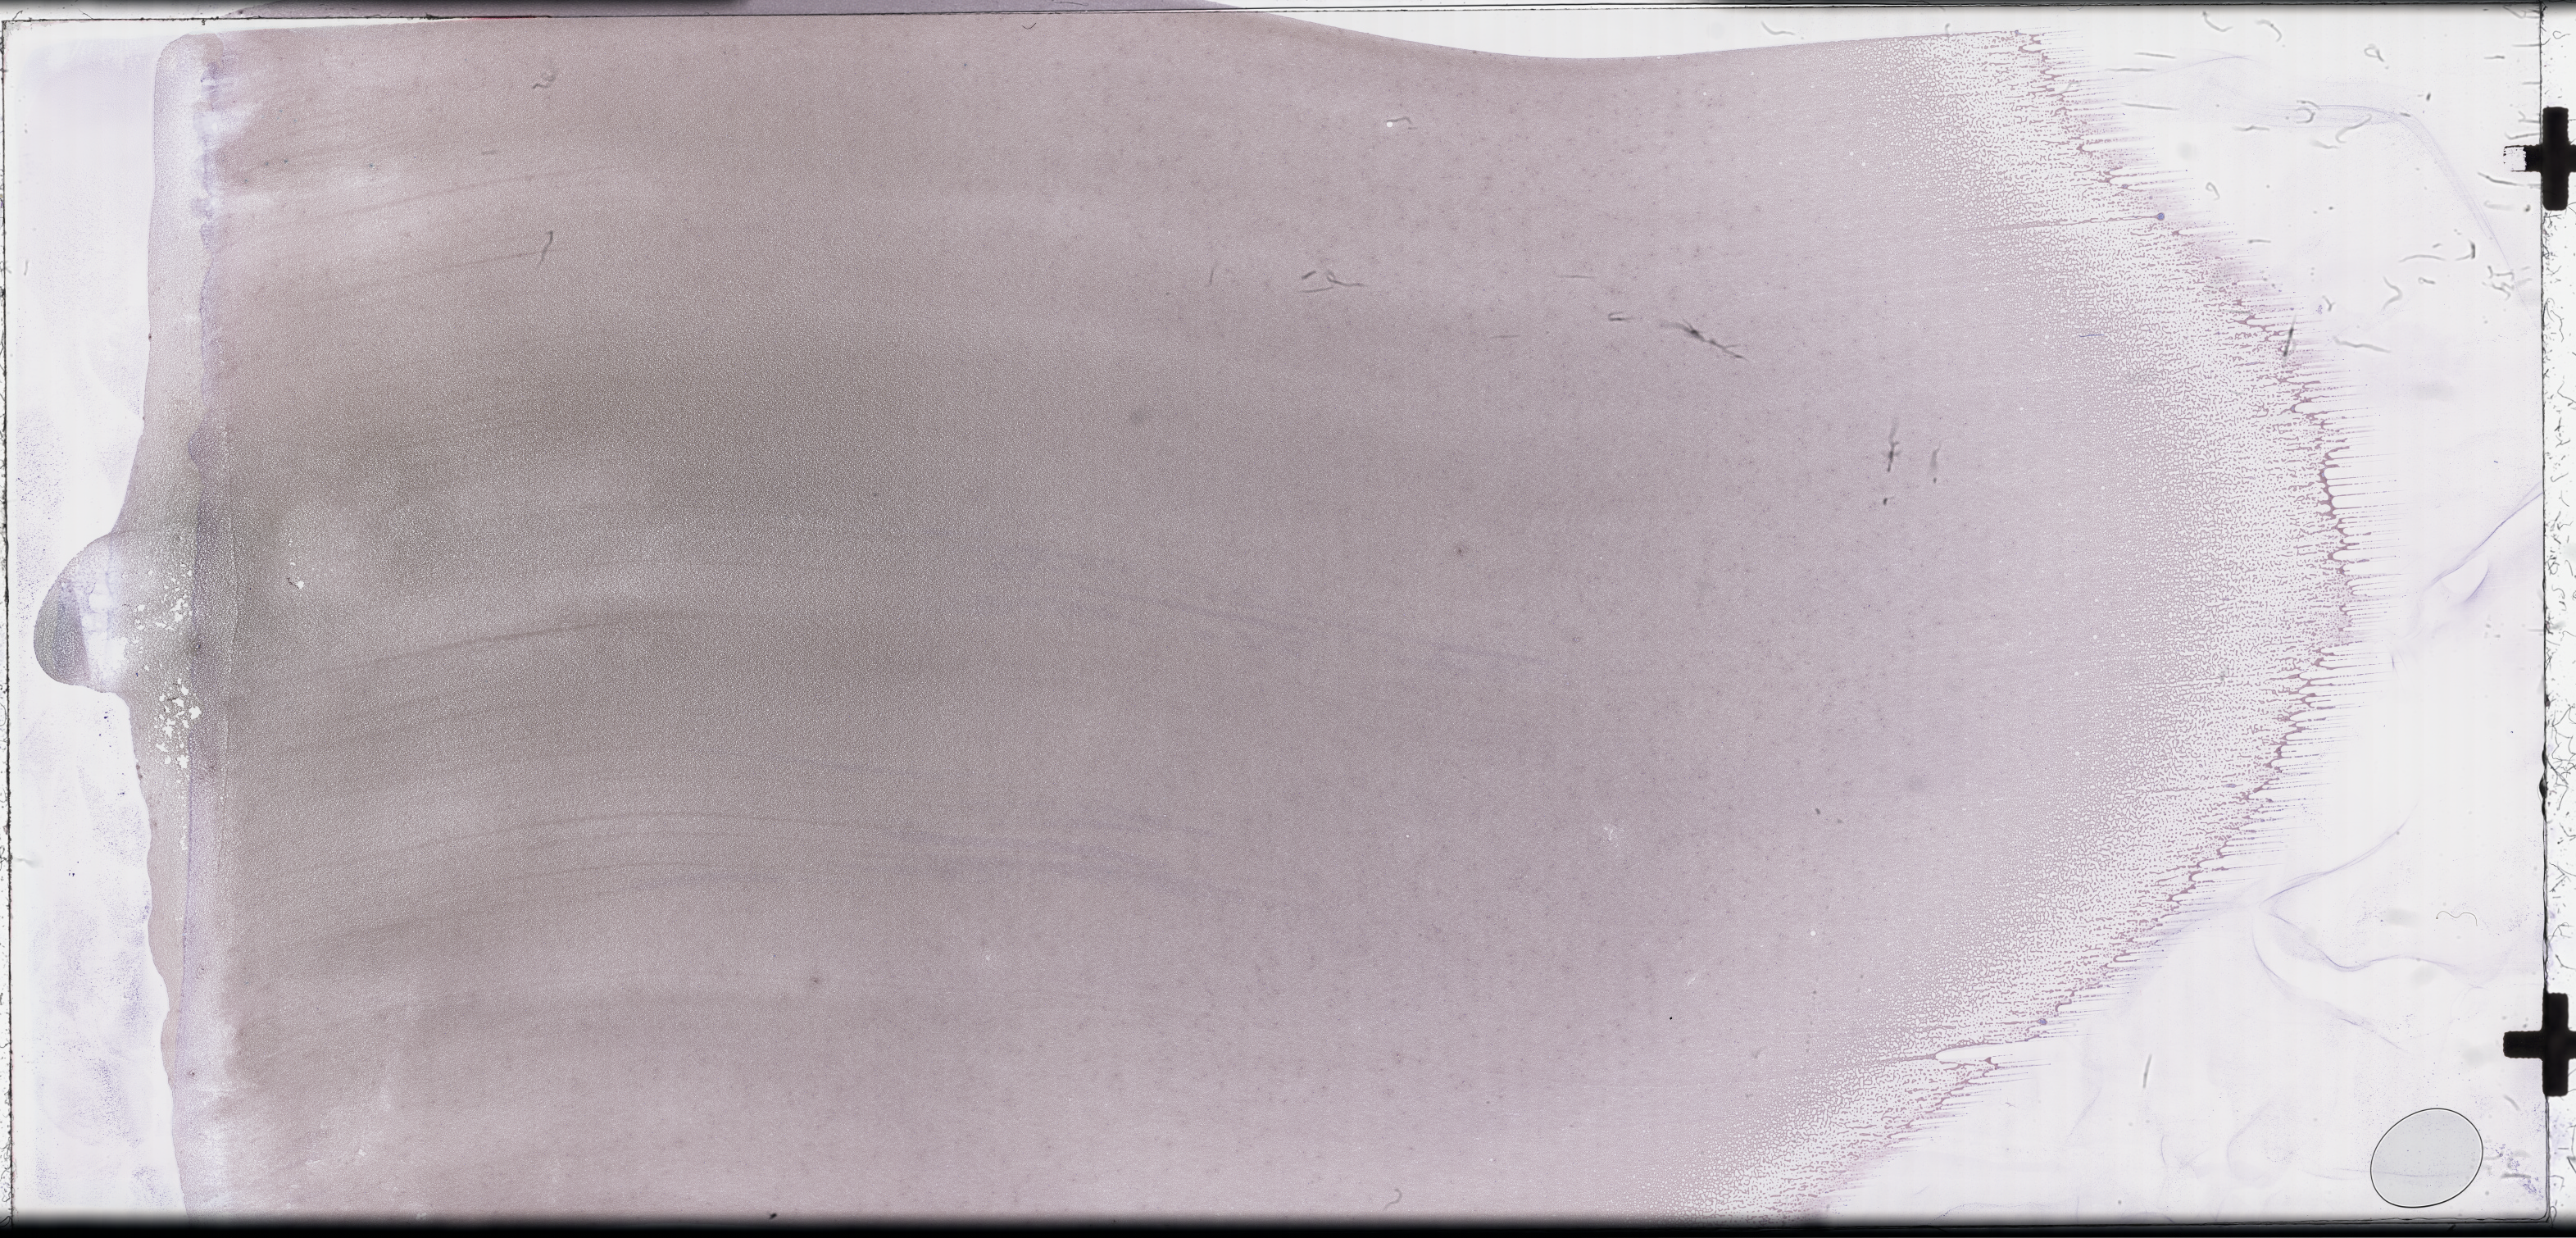
Whole-slide image of a whole blood smear, Wright–Giemsa stain — shown as a low-resolution overview of the whole scanned area (about 50.8 x 24.4 mm), smear from an EDTA sample, specimen time point: collected on treatment. Patient: male.
Patient diagnosis: Plasma Cell Myeloma.